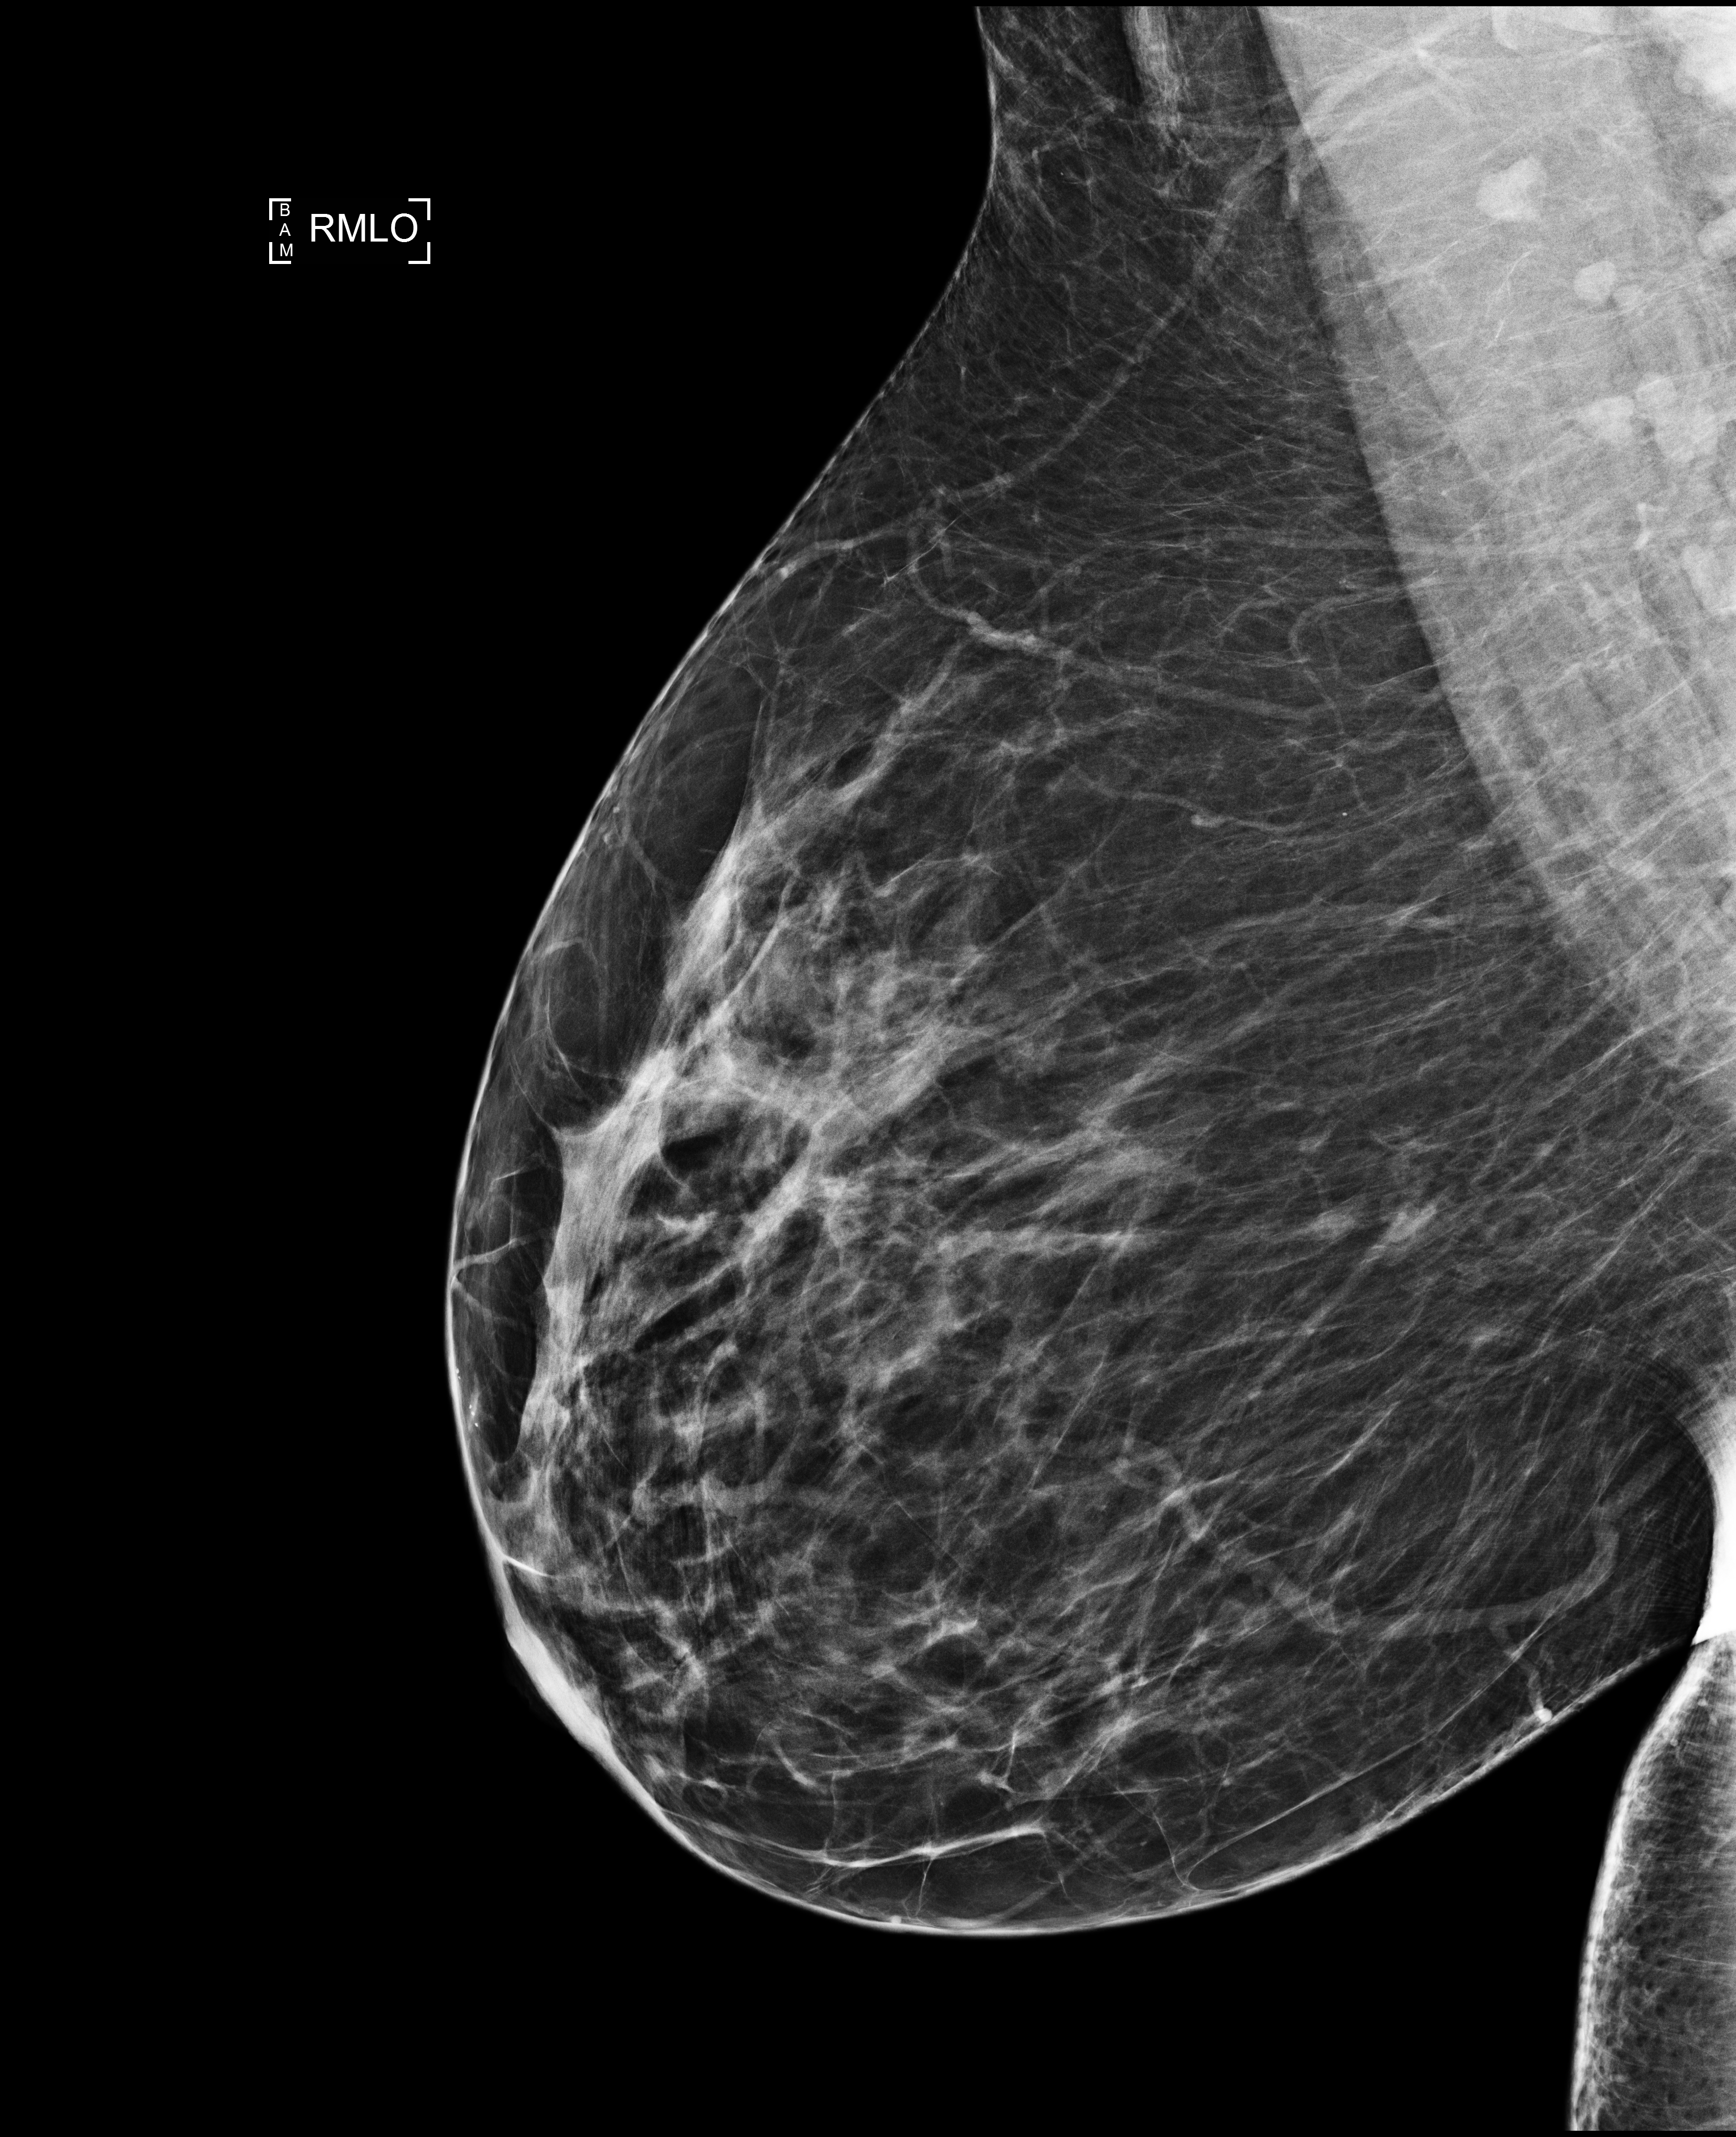
Screening examination; system: Selenia Dimensions. Patient aged 47 years (female).
Image type: full-field digital mammogram. Breast: right. Projection: medio-lateral oblique projection.